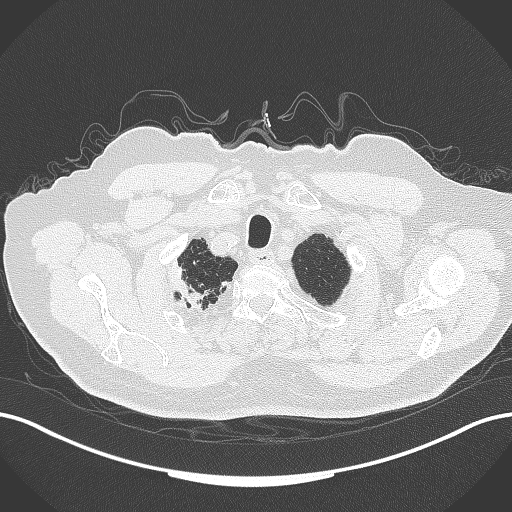
Chest CT, one axial slice. Slice 333 of 389 in the series (ordered by position). 120 kVp. Lung window (W 1500 / L -600 HU). 512 × 512 image matrix, field of view 400 × 400 mm. Male patient, age 72 years. Case-level facts recorded for this patient, not image findings: clinical TNM (as recorded): T1a N0 M0.
Outlined on this slice (bounding box drawn by a radiologist):
- lung tumour (recorded histology: squamous cell carcinoma): bounding box (x1, y1, x2, y2) in pixels: (166, 257, 212, 314)